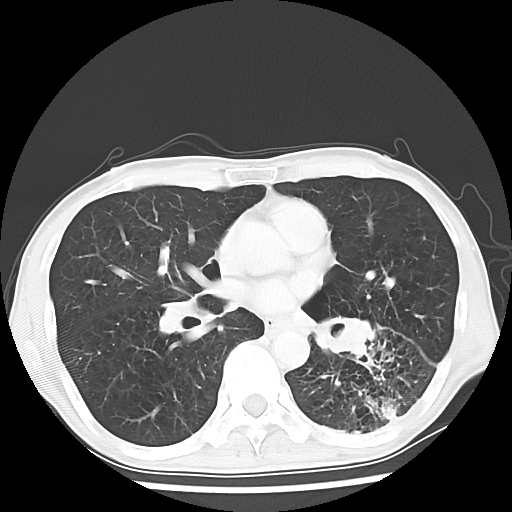
Chest CT, one axial slice. Position 31 of 64 along the scan axis. Reconstruction kernel LUNG. 120 kVp. Lung window (W 1500 / L -600 HU). 5 mm slice thickness. 512 × 512 image matrix, field of view 313 × 313 mm. Patient: male, 68 years. Case-level facts recorded for this patient, not image findings: clinical TNM (as recorded): T4 N0 M0.
Annotated regions visible in this slice (rectangle marked by the reading radiologist):
- lung tumour (recorded histology: squamous cell carcinoma): bounding box [x1, y1, x2, y2] px = [303, 308, 381, 361]